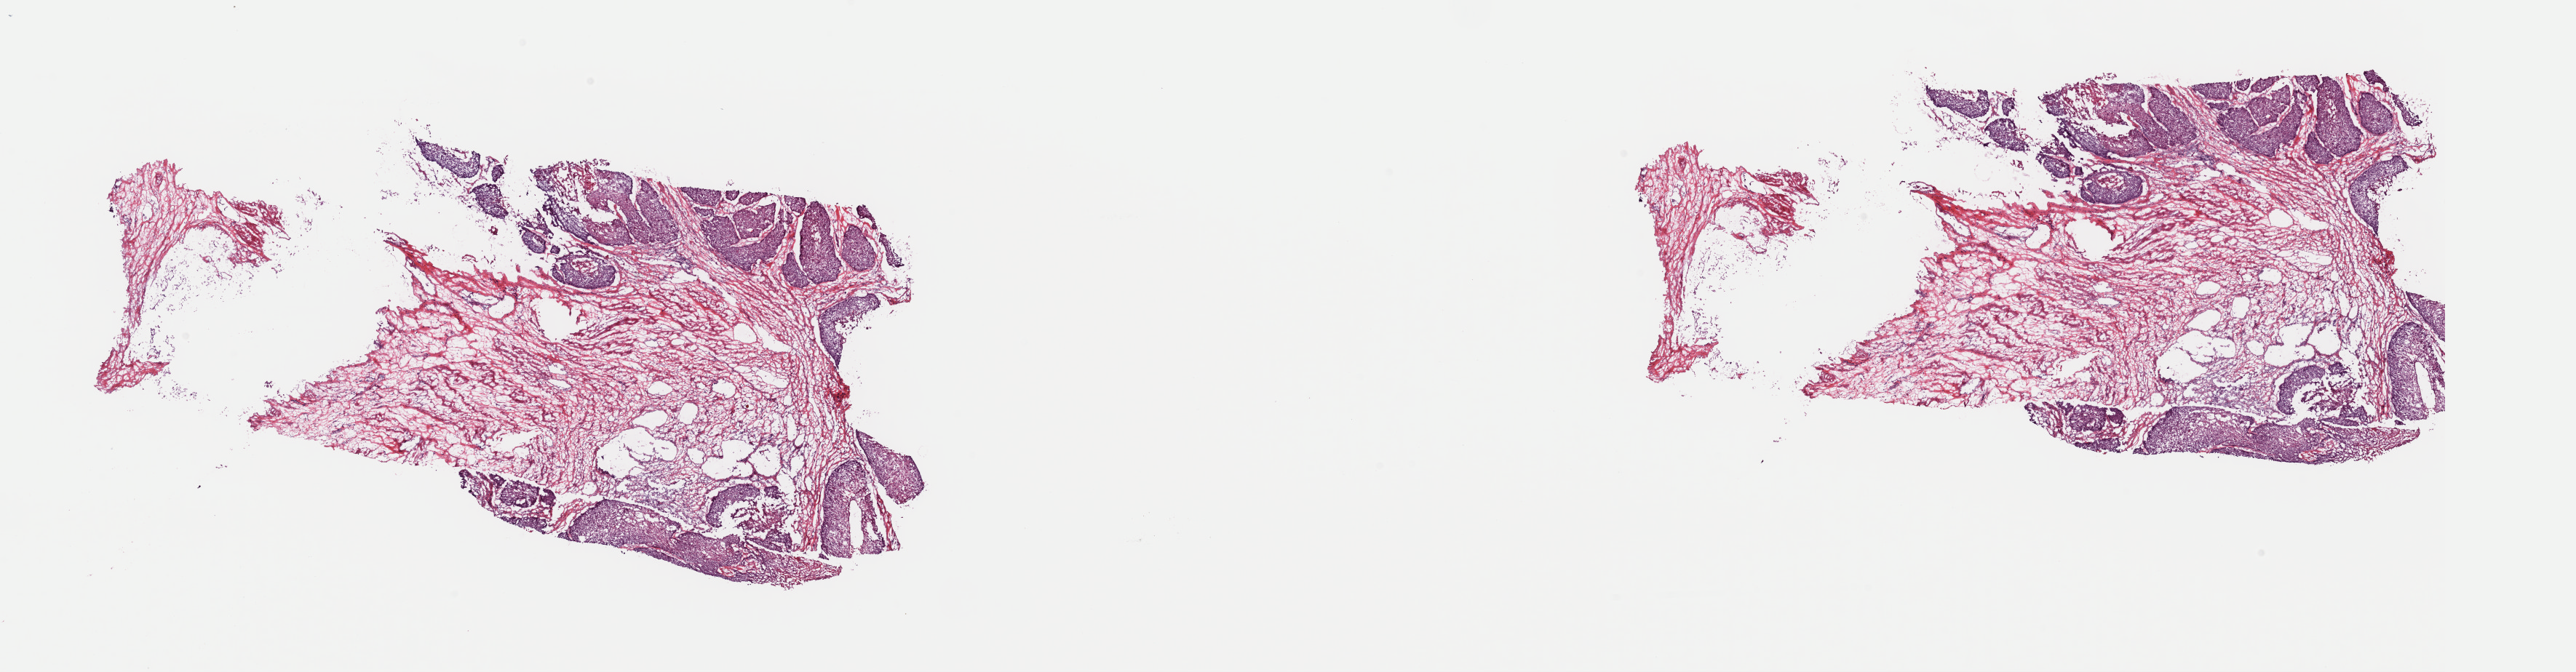
Whole-slide histology image, H&E — a low-resolution overview of the entire scanned area, about 28.0 x 7.3 mm. Frozen section. Primary tumour sample from the esophagus. Male patient; age at initial diagnosis 58 years. Histologic grade: G1 (well differentiated). Composition of this section per pathologist review: tumour cells 20%, tumour nuclei 70%, normal cells 0%, stromal cells 75%, necrosis 5%. Infiltration values recorded for this section: lymphocyte infiltration 10%, monocyte infiltration 5%, neutrophil infiltration 3%.
AJCC pathologic stage: IIA. Diagnosis: Squamous cell carcinoma, NOS (middle third of esophagus).